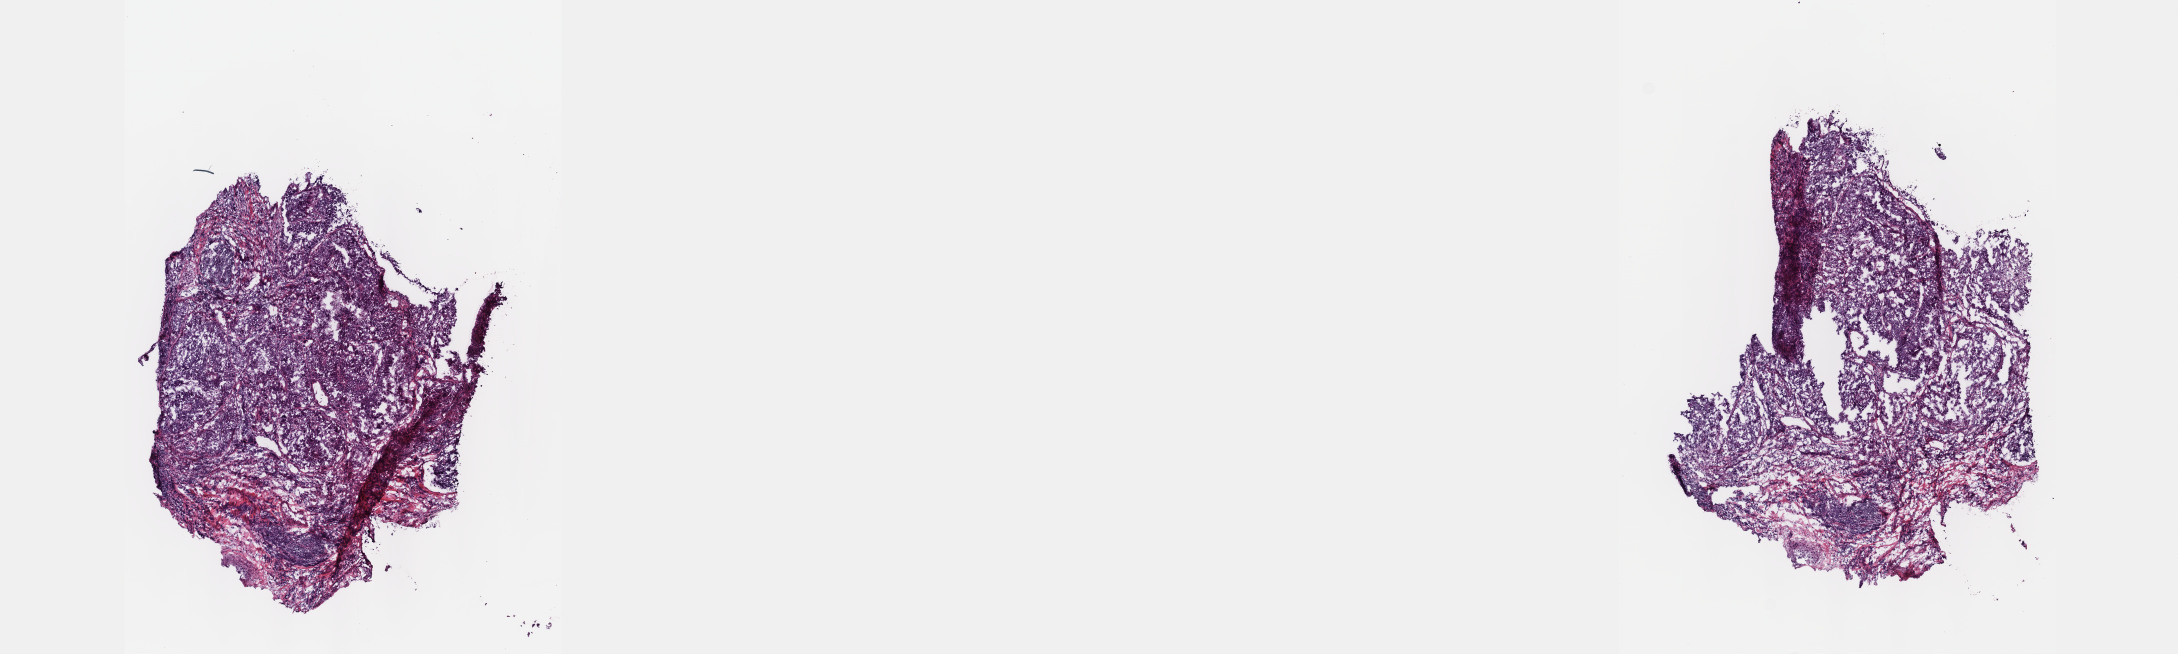
H&E-stained whole-slide image, low-resolution overview of the scanned area, about 17.6 x 5.3 mm, frozen section, sample: primary tumour, lung. Patient: female, age at initial diagnosis 65 years. Slide review estimates, as recorded: tumour cells 40%, tumour nuclei 65%, normal cells 10%, stromal cells 30%, necrosis 20%. Infiltration values recorded for this section: lymphocyte infiltration 25%, monocyte infiltration 6%, neutrophil infiltration 3%.
TNM: T2 N1 MX. Pathologic diagnosis: Squamous cell carcinoma, NOS (upper lobe, lung). AJCC pathologic stage: IIB.